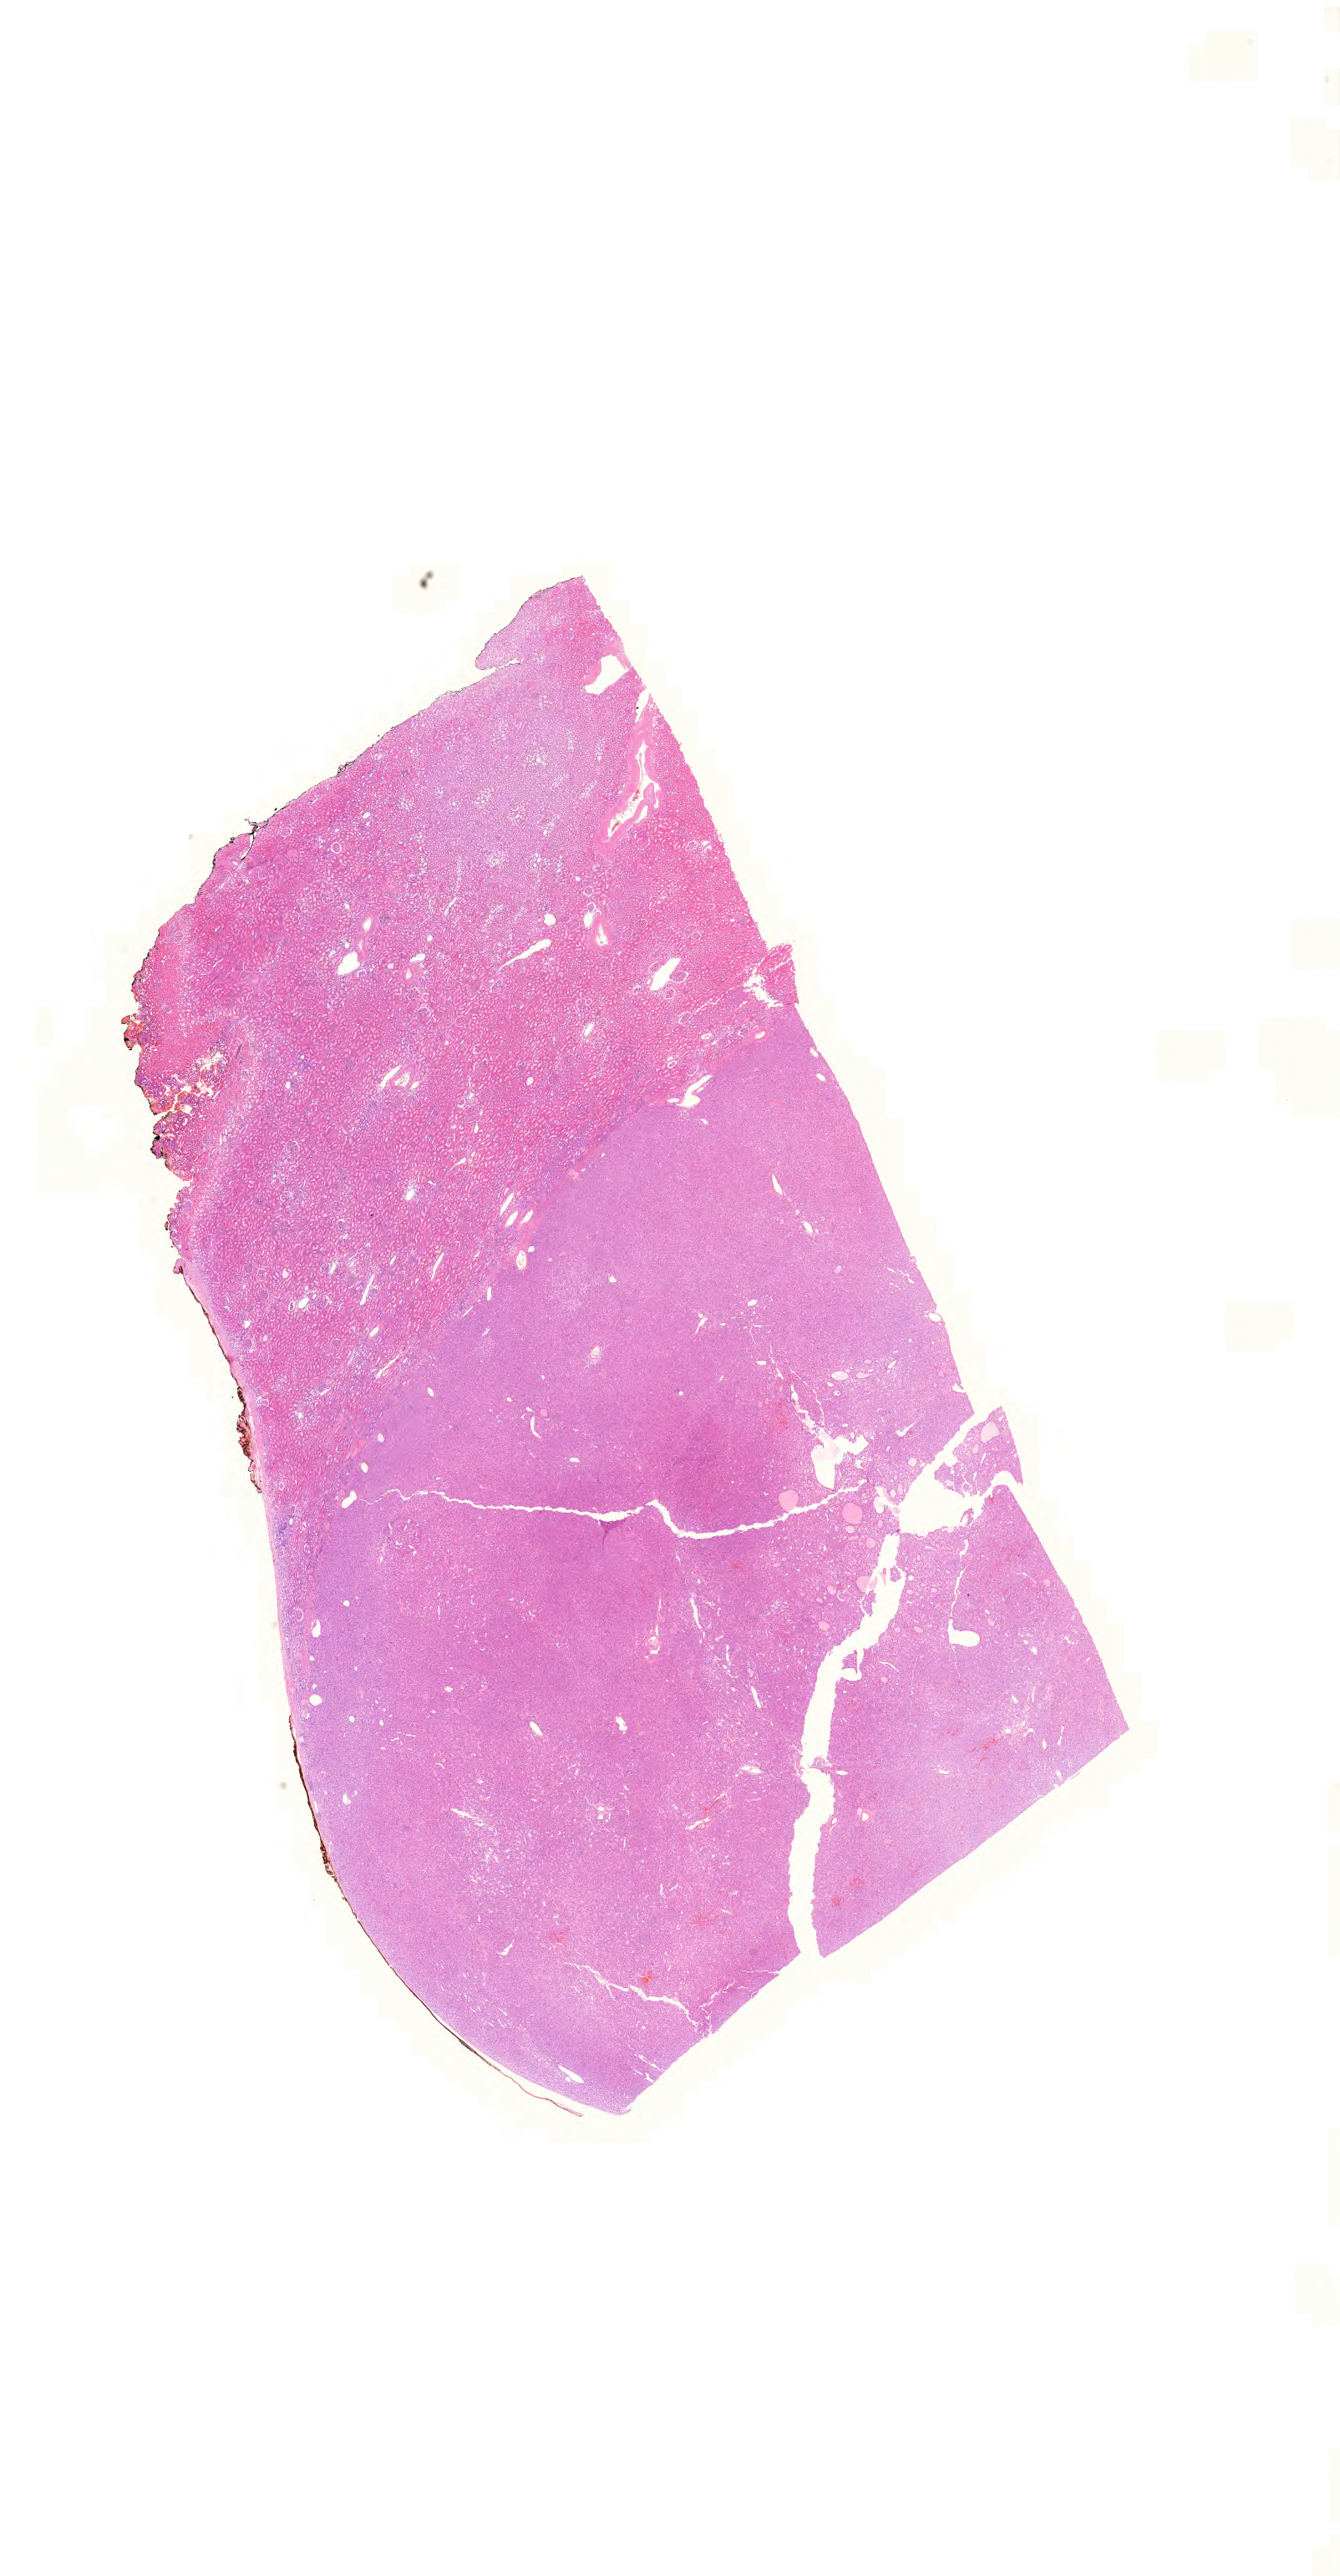
H&E-stained whole-slide image, low-resolution overview of the scanned area, about 23.9 x 45.9 mm, formalin-fixed paraffin-embedded (FFPE) diagnostic section, primary tumour sample from the kidney. Female, age 47 years at initial diagnosis. Histologic grade: G1 (well differentiated).
- diagnosis: Clear cell adenocarcinoma, NOS
- AJCC pathologic stage: I (7th edition)
- TNM: T1a NX MX